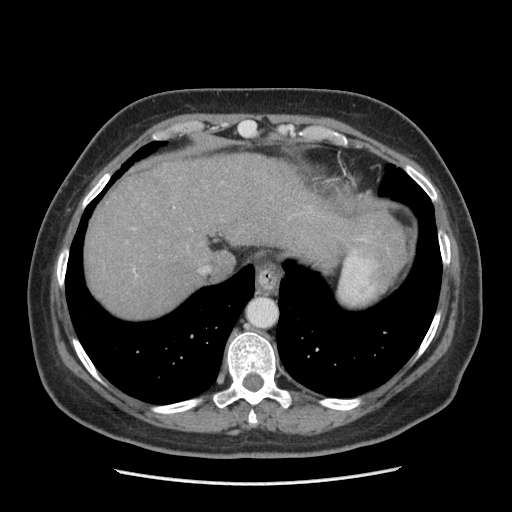
Contrast-enhanced abdominal CT (liver protocol), one axial slice; slice 168 of 185 in the series (ordered by position); reconstruction kernel STANDARD; soft-tissue window (W 400 / L 40 HU); 512 × 512 image matrix. From the clinical record (not read from this slice): diagnosis: hepatocellular carcinoma (patient treated with transarterial chemoembolisation; whether this scan precedes or follows treatment is not stated here); TNM stage (as recorded): Stage-I; Child-Pugh class: A.
Annotated regions visible in this slice (semi-automatic segmentation, software-assisted and operator-edited):
- liver parenchyma outside the tumour (the mass and vessels are separate outlines, so this box may not span the whole liver): bounding box [x1, y1, x2, y2] px = [86, 152, 406, 318]